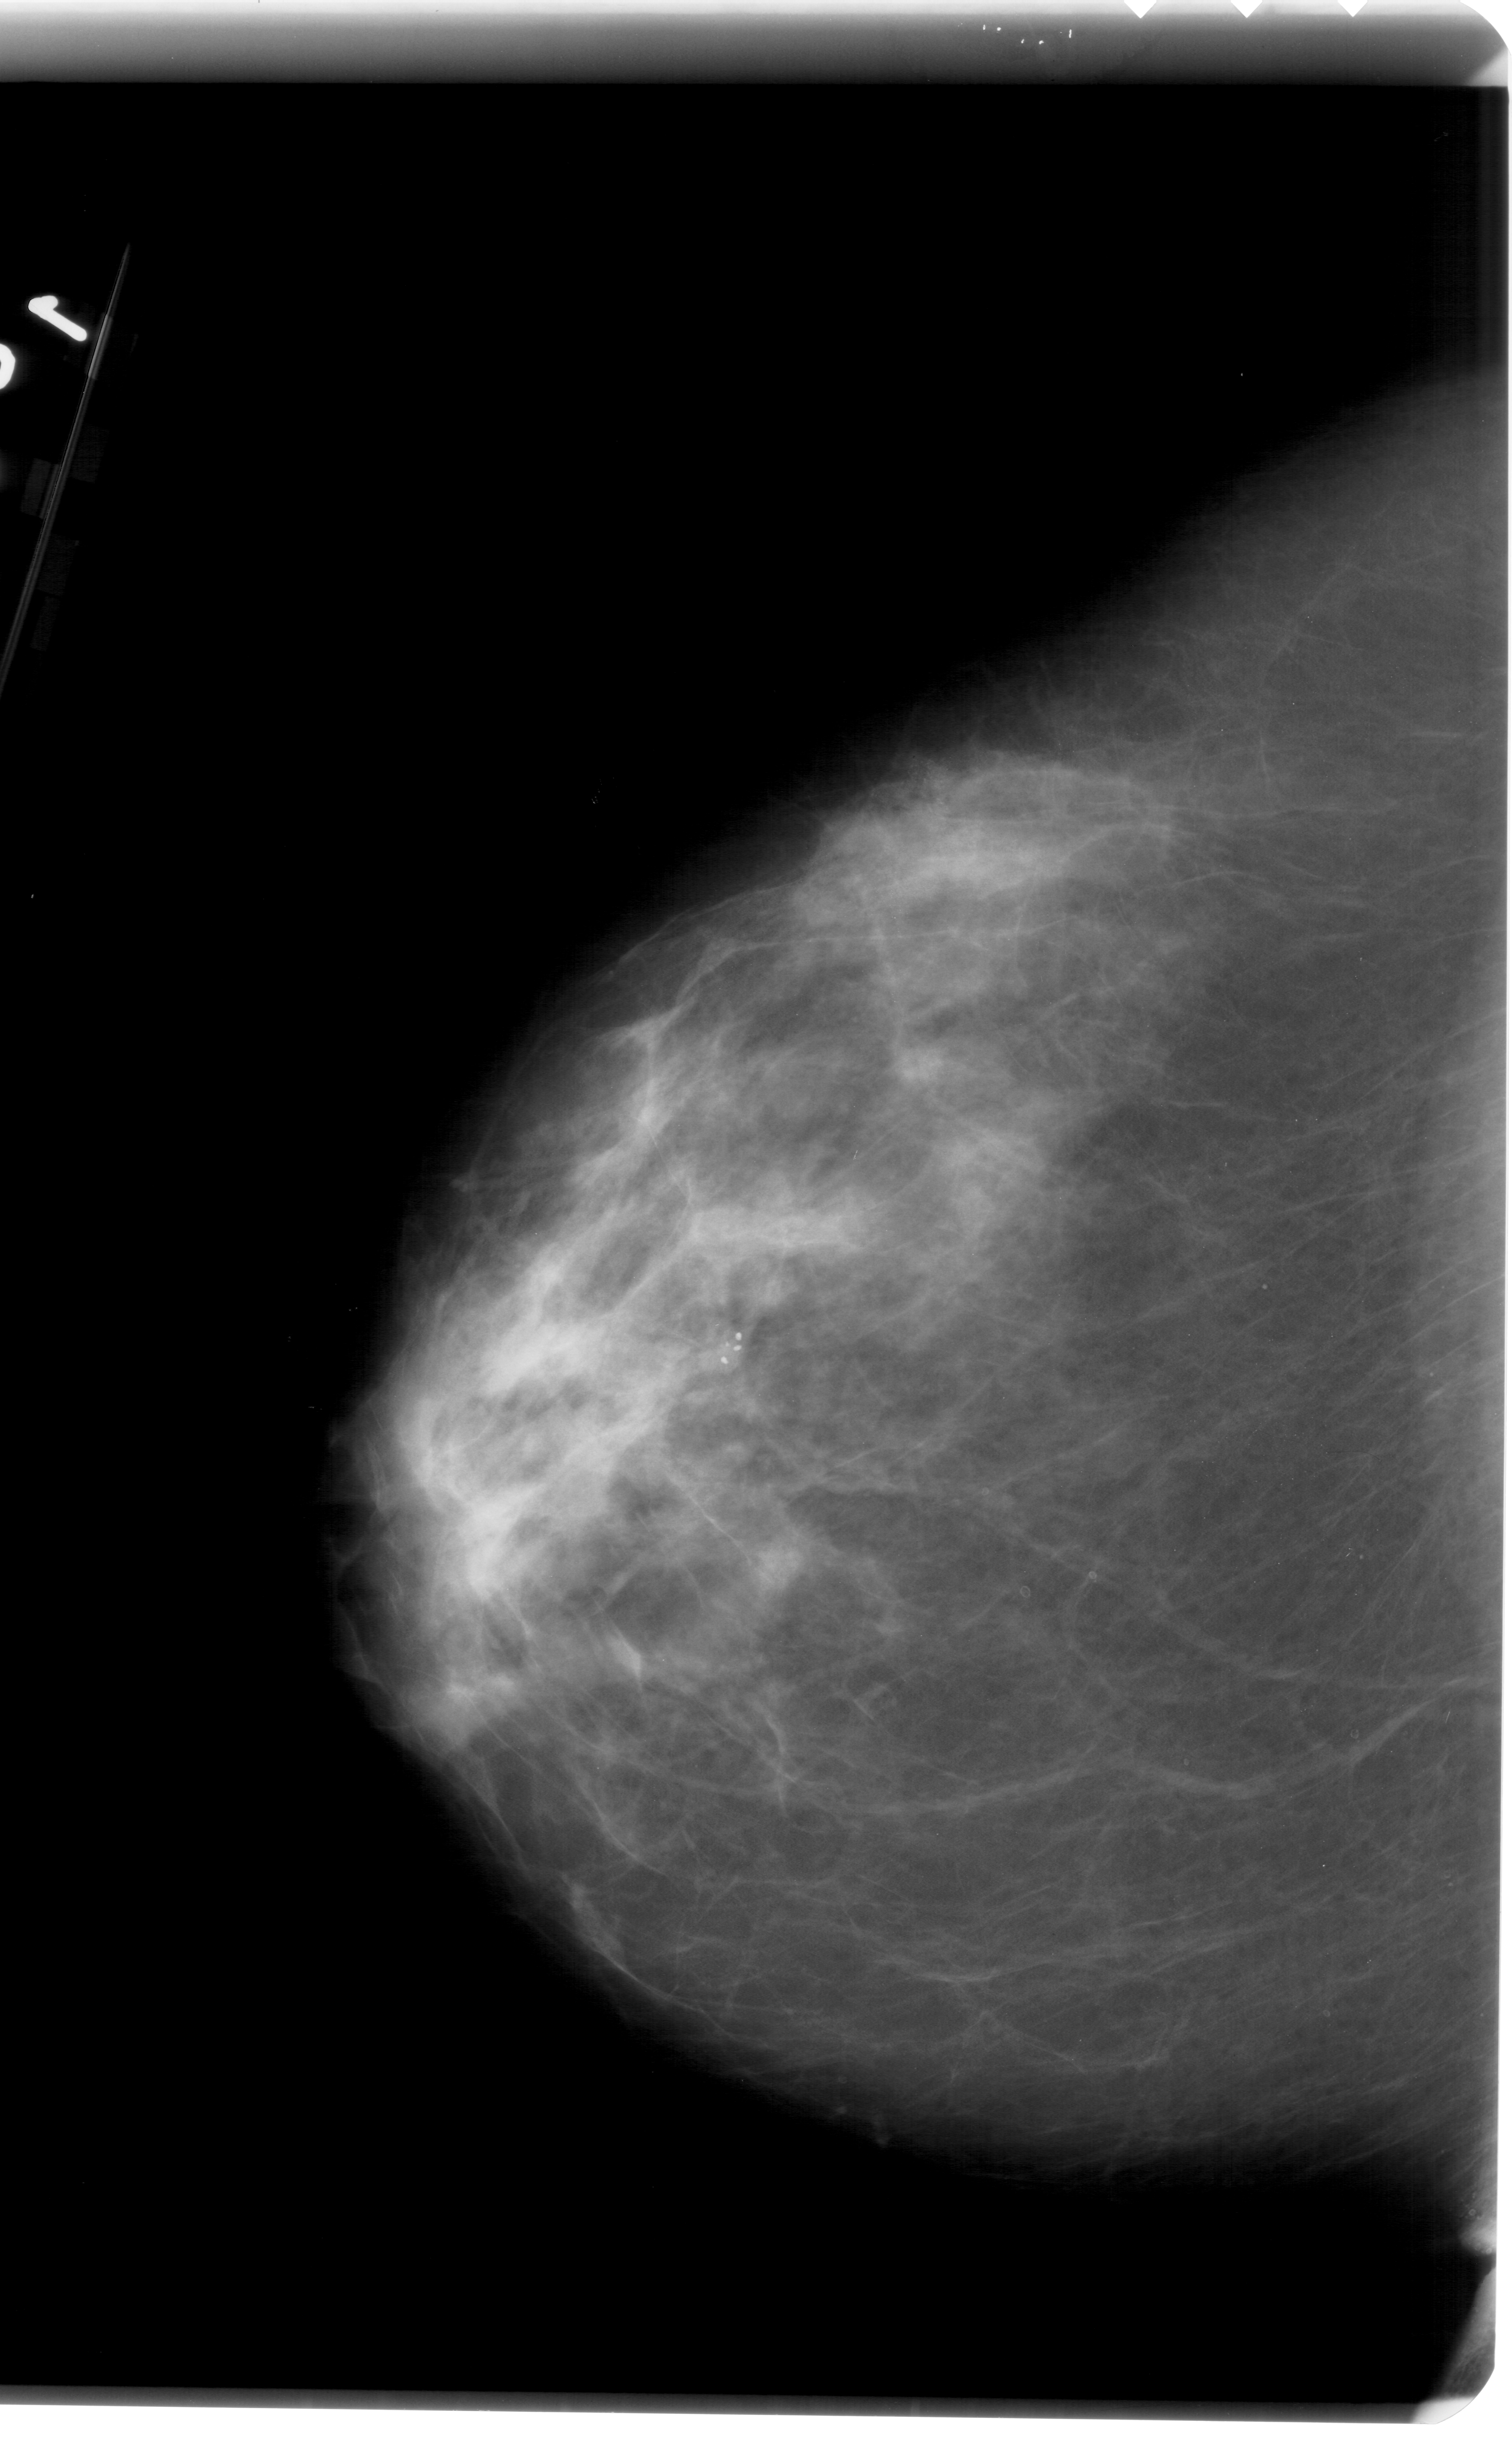
Scanned film-screen mammogram. Left breast. Craniocaudal (CC) view. BI-RADS breast density category 4 (scale 1–4). 1512 × 2456 image matrix.
Marked abnormalities (boxes around the expert regions of interest):
- calcifications, morphology pleomorphic, distribution clustered; BI-RADS assessment category 4; subtlety rating 2 on a 1 (subtle) to 5 (obvious) scale; pathology (as recorded): malignant: bounding box <906,744,993,852> (left, top, right, bottom; pixels)